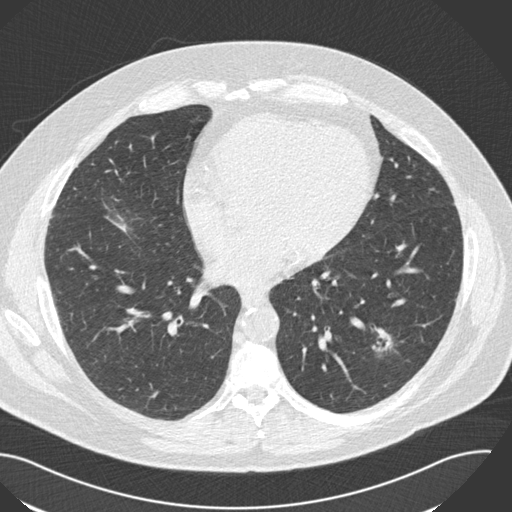
Axial slice from a low-dose chest CT screening exam. Third annual screen. Lung window (W 1500 / L -600 HU). 2 mm slice thickness. Standard (soft-tissue) reconstruction kernel (B30f). Slice 80 of 153 in the series. Male participant, aged 57 years at enrolment. Current smoker at enrolment.
• Lesion marked by an expert reader, box from (x=348, y=314) to (x=416, y=370) px.
• Screening reader's record for this exam (one nodule recorded; not confirmed to be the boxed lesion): non-calcified nodule or mass ≥4 mm, left lower lobe, 22 × 18 mm, poorly defined margins, soft tissue attenuation, pre-existing on the prior screen: yes; interval growth: yes.
• Official screen result: positive, other.
• Participant outcome: lung cancer diagnosed 124 days after this screen — squamous cell carcinoma, NOS, left lower lobe, moderately differentiated (G2), stage IA (AJCC 6th edition), 22 mm at pathology.